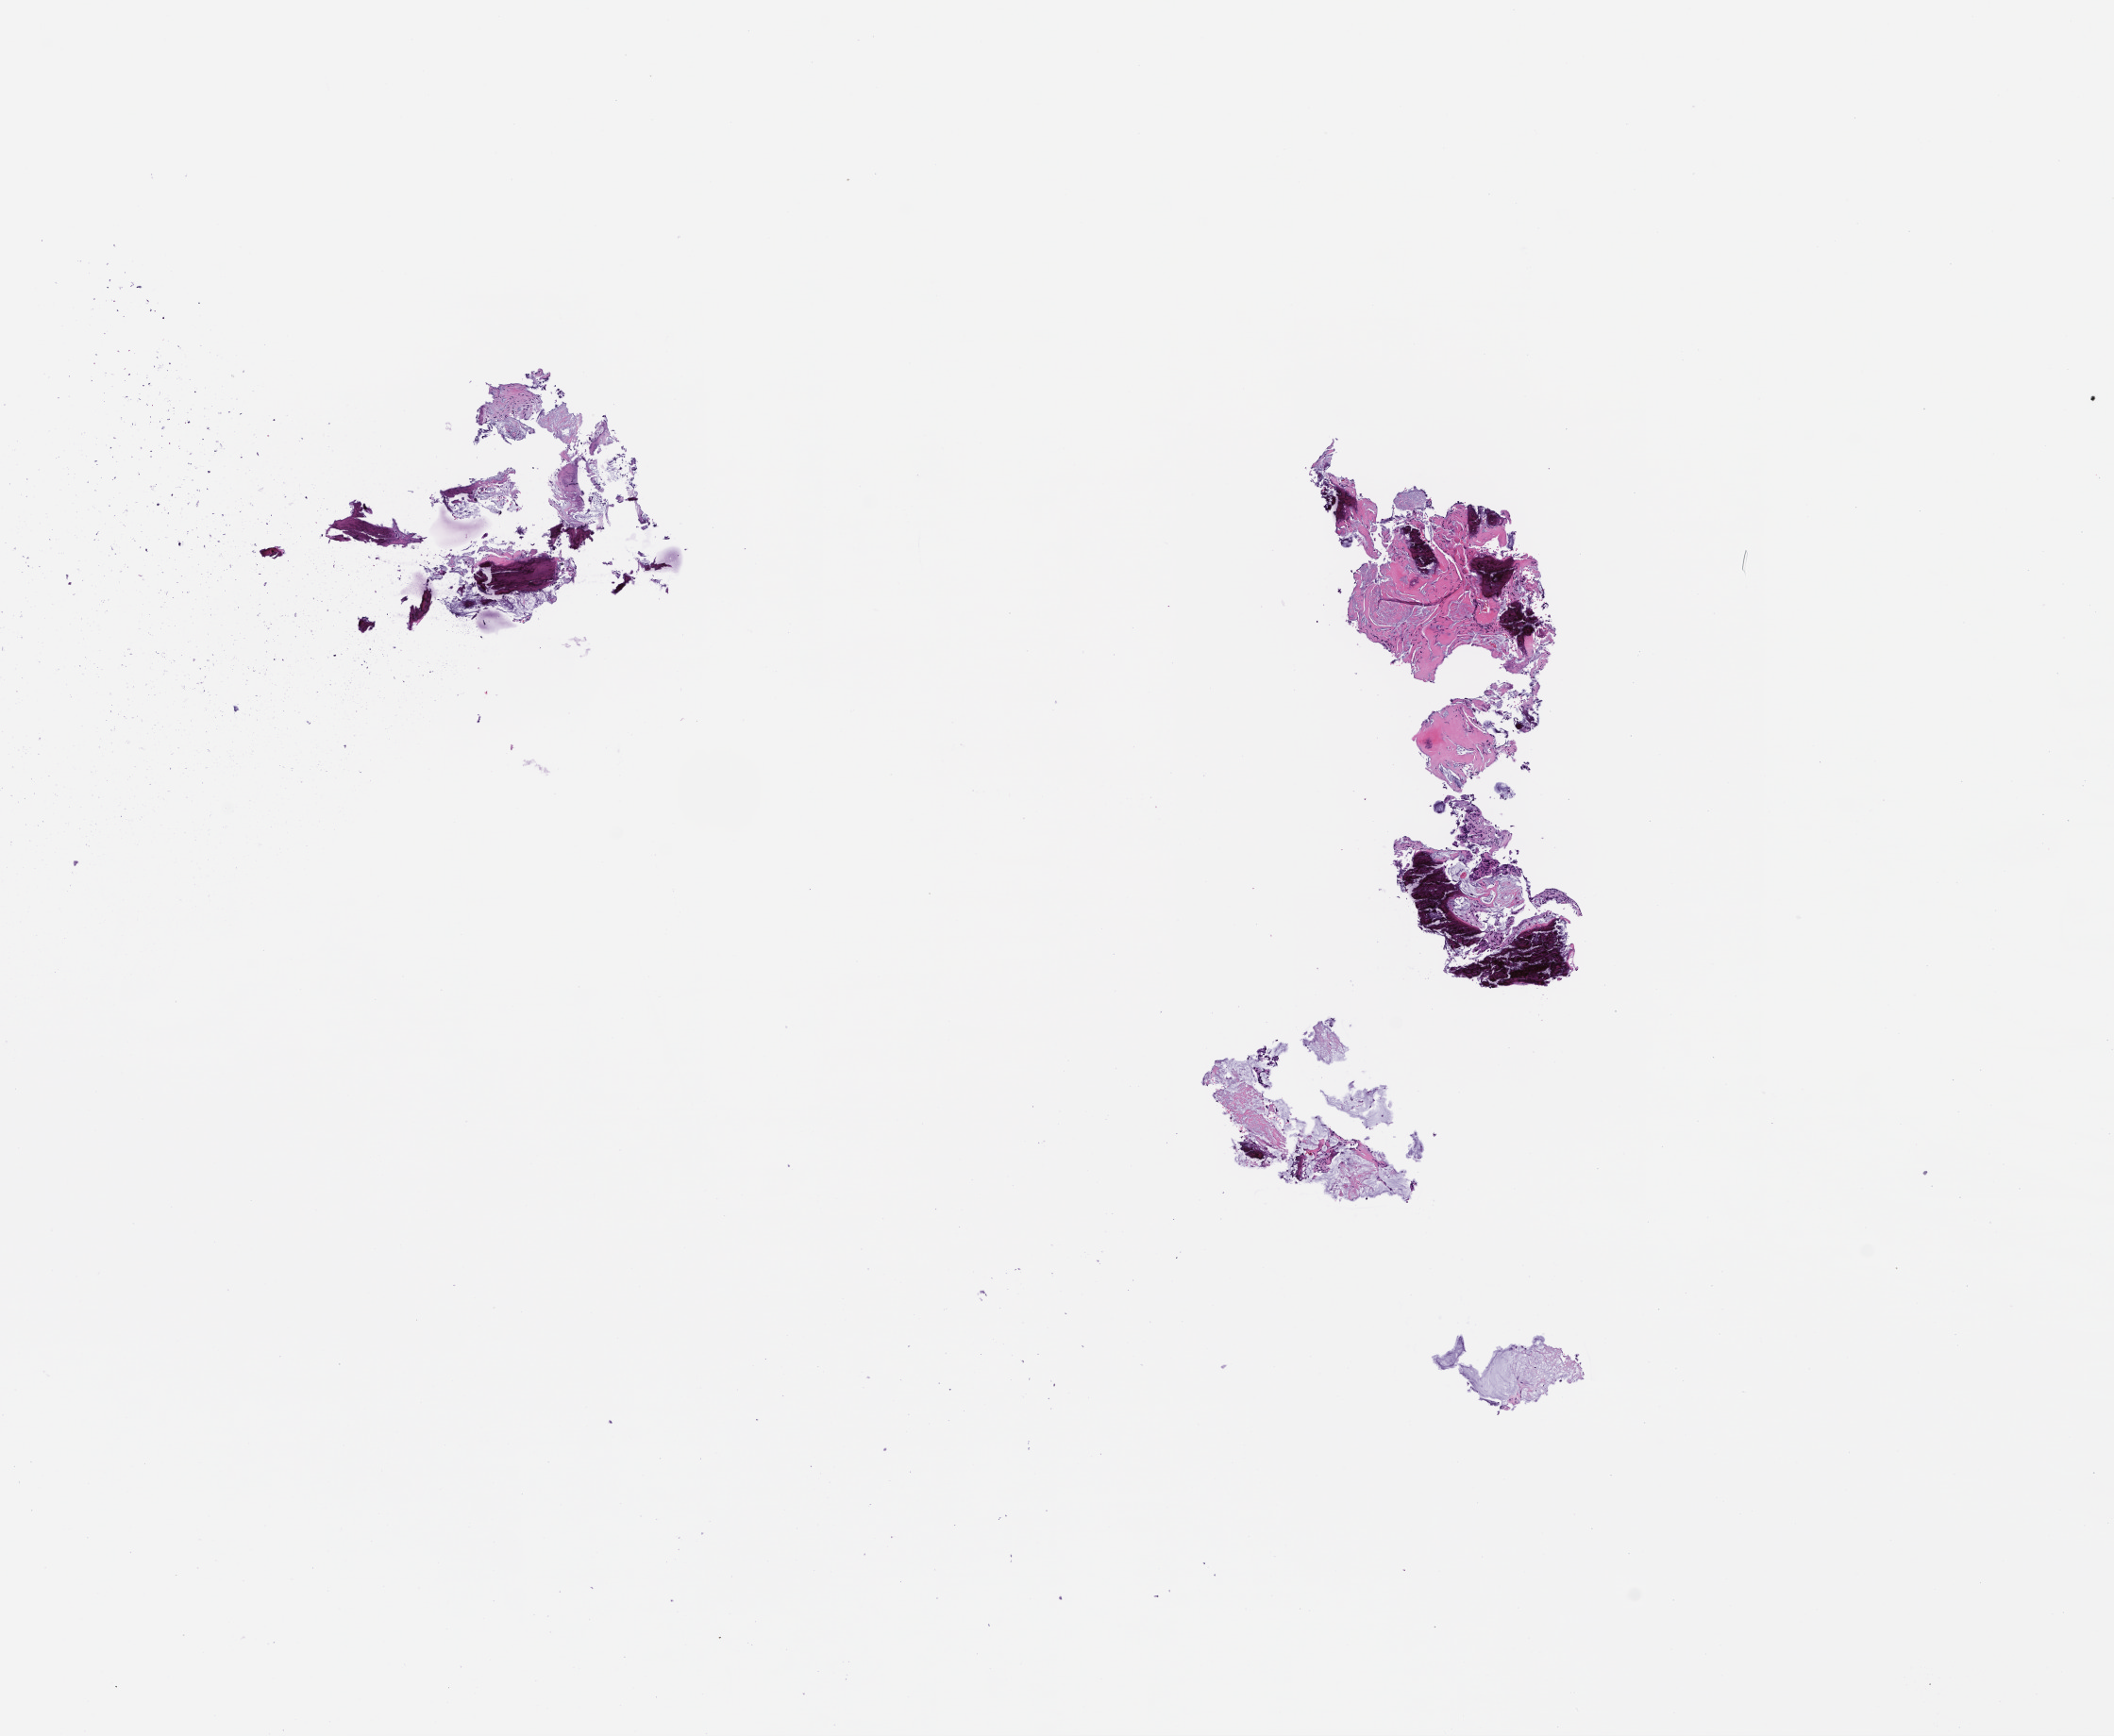
Whole-slide image, H&E stain — low-resolution overview of the scanned area, about 9.0 x 7.4 mm; formalin-fixed paraffin-embedded section; collected at disease progression. Patient sex: female.
* this section: metastatic tumor tissue
* primary diagnosis of the patient: Colorectal Carcinoma